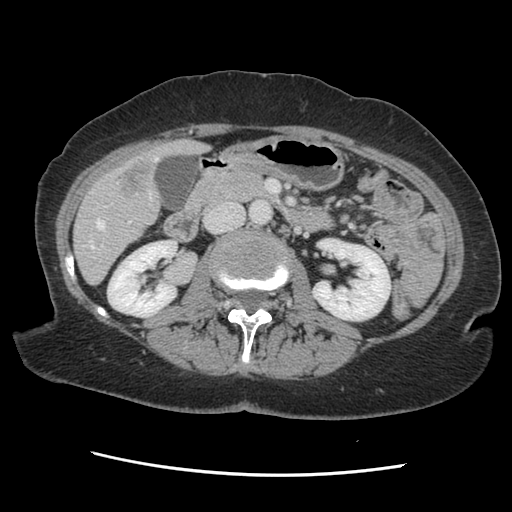
Contrast-enhanced abdominal CT, one axial slice. Slice 57 of 141 in the series (ordered by position). Soft-tissue window (W 400 / L 40 HU). 2.5 mm slice thickness. 512 × 512 image matrix, field of view 330 × 330 mm. Female patient, age 61 years. Case-level facts recorded for this patient, not image findings: diagnosis: colorectal cancer liver metastases, imaged before liver resection; multiple liver metastases: no; largest metastasis: 2.4 cm.
Annotated regions visible in this slice (manually delineated by an expert):
- hepatic veins: box from (x=84, y=158) to (x=158, y=249) px
- liver: (x=74, y=140)–(x=205, y=283)
- planned liver remnant (the part of the liver to remain after resection): (x=74, y=193)–(x=159, y=283)
- portal vein (with intrahepatic branches): (x=102, y=182)–(x=130, y=247)
- liver metastasis: (x=118, y=161)–(x=153, y=197)